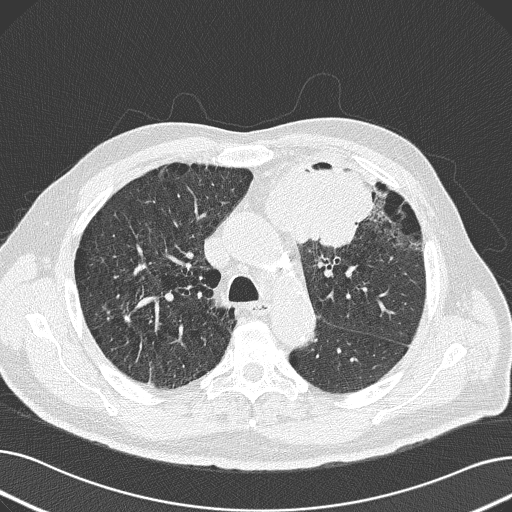
Axial slice from a low-dose chest CT screening exam. Baseline screening round. Lung window (W 1500 / L -600 HU). 2 mm slice thickness. Slice 59 of 165 in the series. 512 × 512 image matrix. Male participant, aged 69 years at enrolment.
- Expert-annotated lung lesion, box from (x=228, y=145) to (x=380, y=253) px.
- Reader record for this screening exam (exam-level; its link to the box is not recorded): non-calcified nodule or mass ≥4 mm, left upper lobe, 6 × 10 mm, spiculated (stellate) margins, soft tissue attenuation.
- Later outcome: lung cancer diagnosed 20 days after this screen — non-small cell carcinoma, left upper lobe, poorly differentiated (G3), stage IB (AJCC 6th edition), 100 mm at pathology.